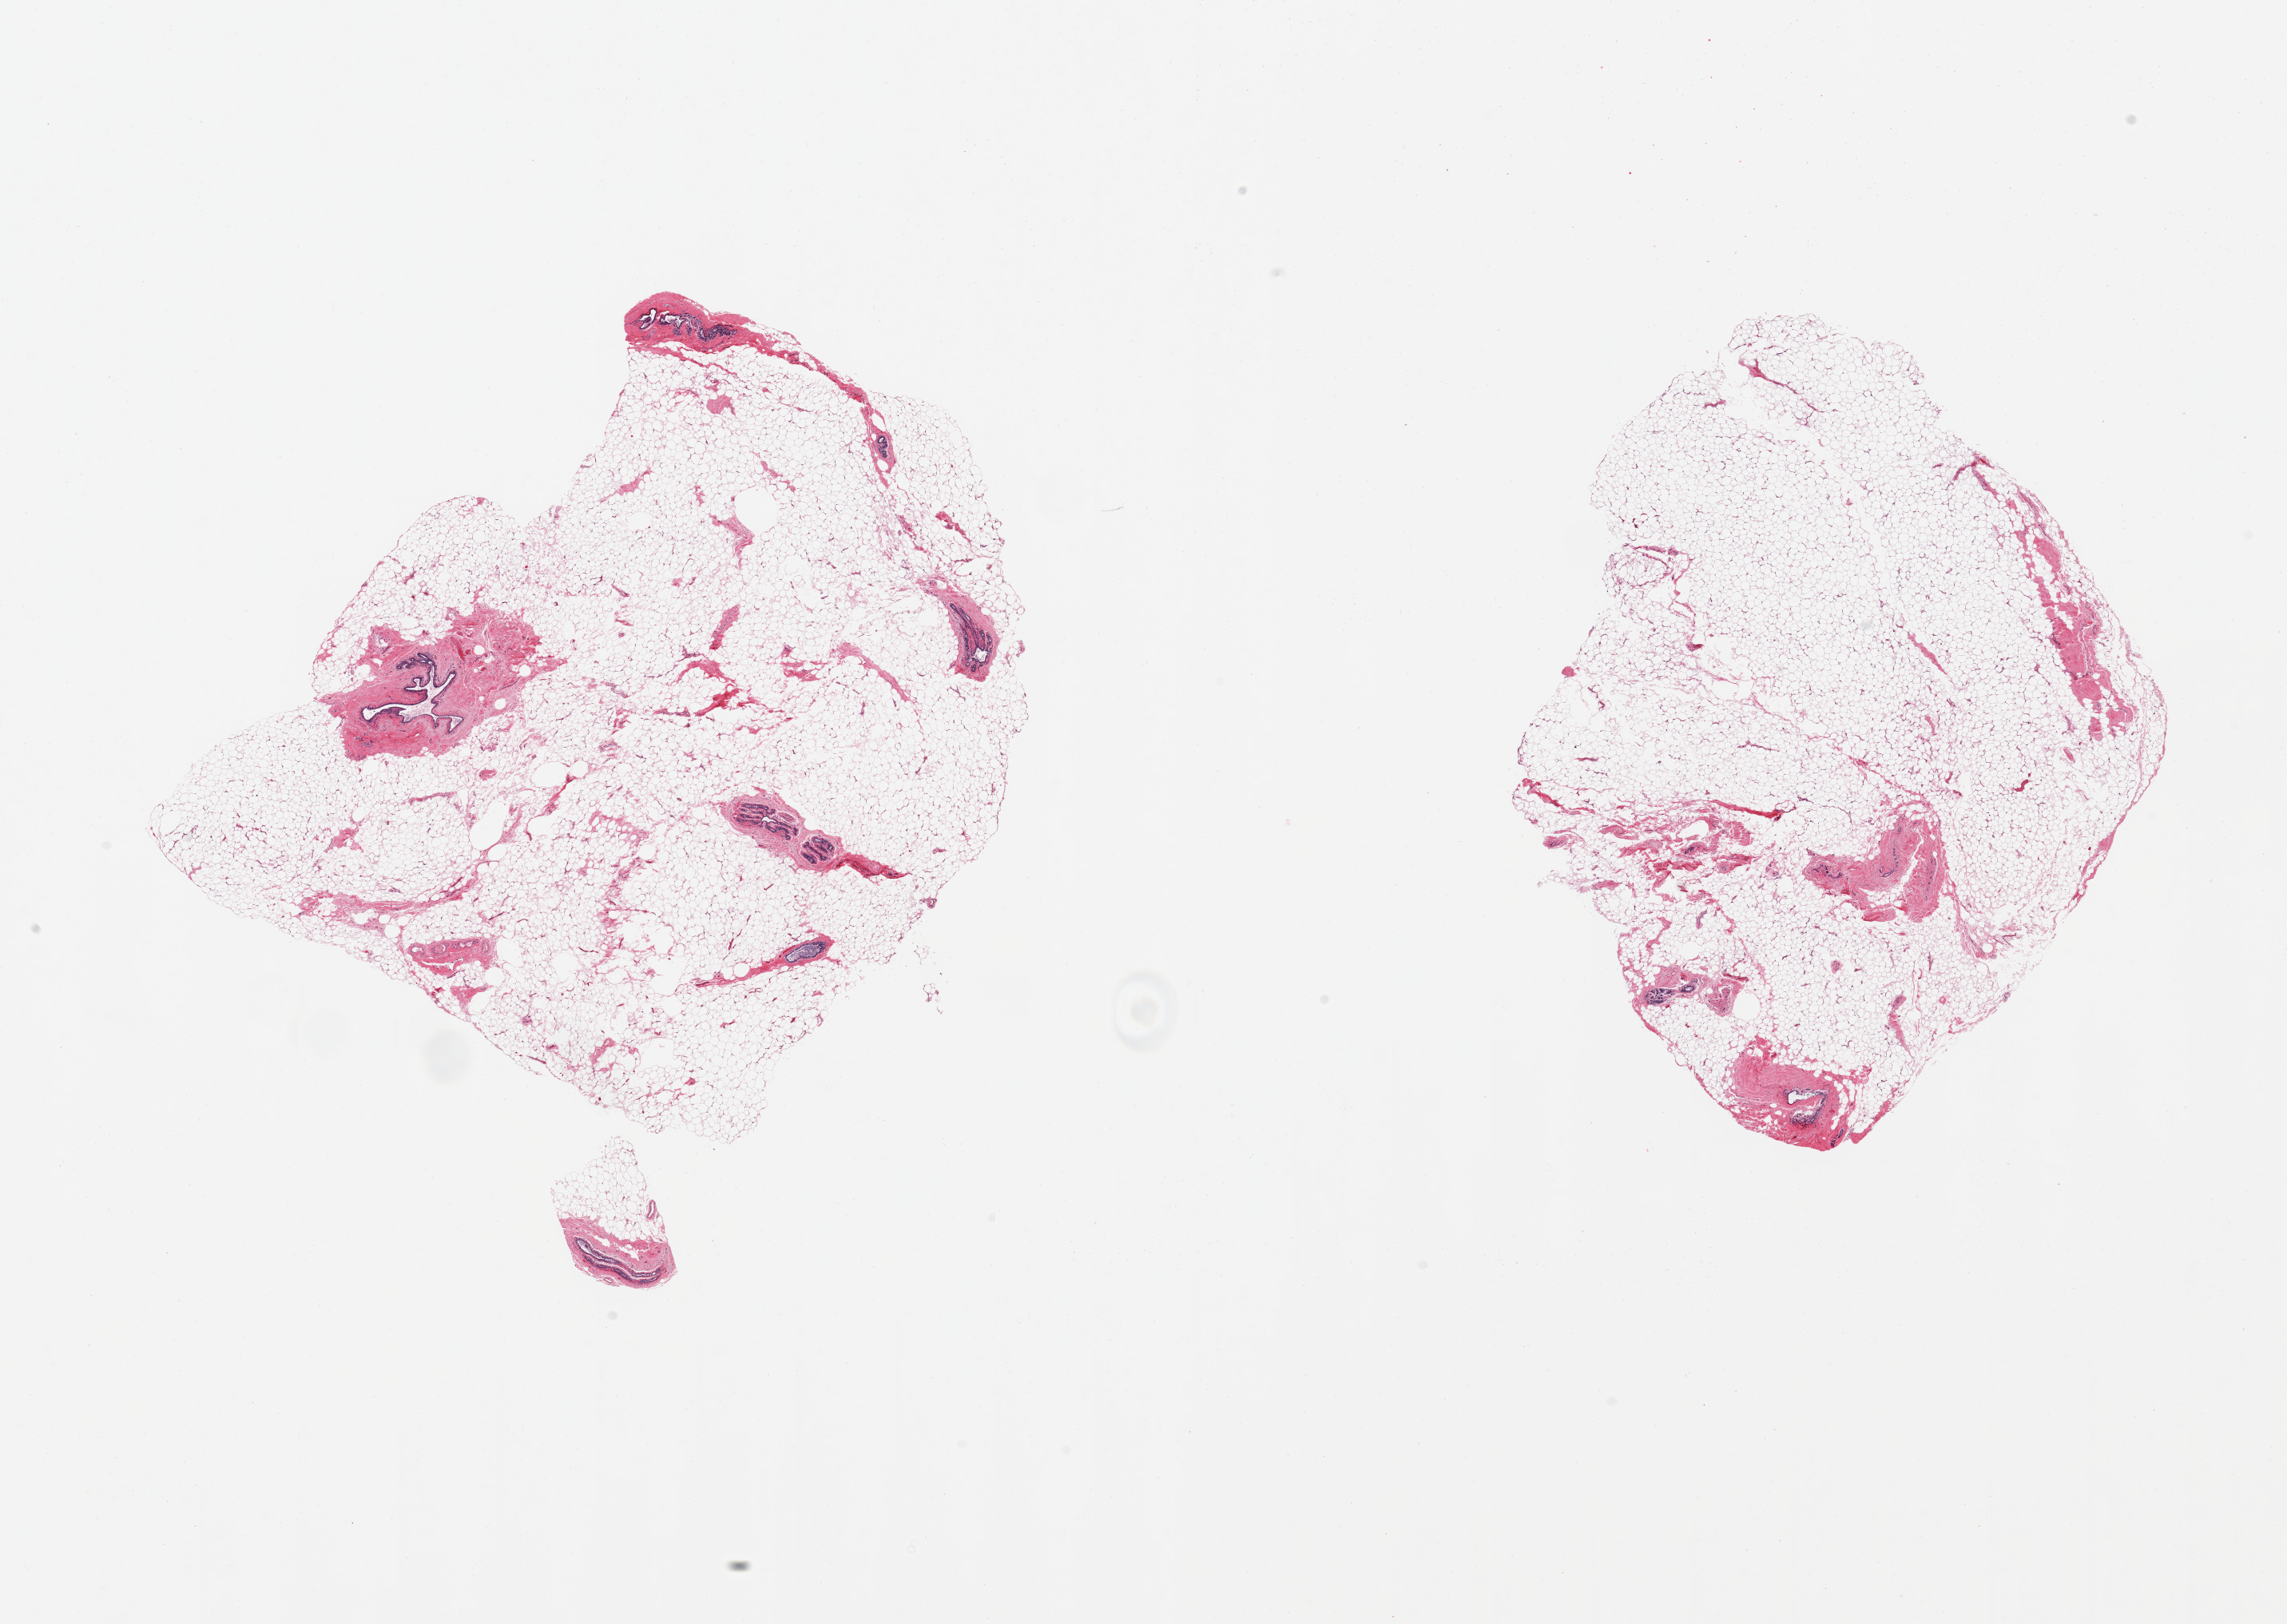
Digitized H&E-stained section — low-resolution overview of the scanned area, about 22.6 x 16.1 mm (from a 20x scan); PAXgene-fixed, paraffin-embedded tissue; target tissue: breast; donor tissue sample.
Pathologist's review note for this sample: 2 pieces, a few atrophic ductal/lobular elements present.